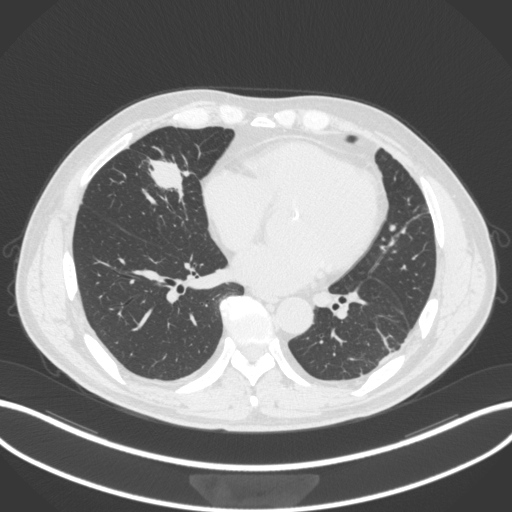
Chest CT, one axial slice. Position 109 of 399 along the scan axis. Reconstruction kernel B31f. 120 kVp. Lung window (W 1500 / L -600 HU). 1 mm slice thickness. 512 × 512 image matrix. Patient: male, 59 years. Case-level facts recorded for this patient, not image findings: clinical TNM (as recorded): T2a N1 M0.
Structures marked on this image (rectangle marked by the reading radiologist):
- lung tumour (recorded histology: adenocarcinoma): bounding box <142,151,193,201> (left, top, right, bottom; pixels)